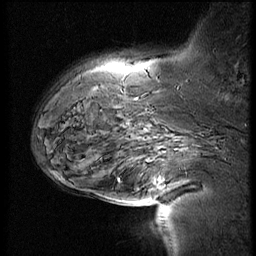
Breast MRI (dynamic contrast-enhanced), one sagittal slice. Slice 17 of 60 in the series (ordered by position). 4 images stored at this slice position (order not interpretable as contrast timing). 1.5 T. TE 4.2 ms, TR 9 ms. 2.5 mm slice thickness. 256 × 256 image matrix, field of view 180 × 180 mm. Female patient, age 56 years. Case-level facts recorded for this patient, not image findings: setting: breast cancer imaged before/during neoadjuvant chemotherapy; receptor status: HER2-positive.
Annotated regions visible in this slice (semi-automatically segmented with operator editing):
- analysis volume of interest (the breast-tissue region the enhancement analysis was run in; not a lesion): bounding box (x1, y1, x2, y2) in pixels: (110, 138, 192, 201)
- tumour enhancement mask (voxels above the 140 % enhancement threshold inside the analysis volume of interest): (158, 179, 160, 181)